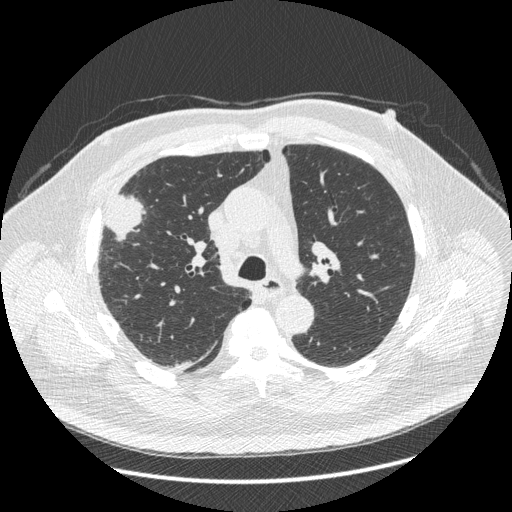
Low-dose screening chest CT, one axial slice; slice 284 of 426 in the series (ordered by position); reconstruction kernel STANDARD; 120 kVp; lung window (W 1500 / L -600 HU); 1.25 mm slice thickness; 512 × 512 image matrix, field of view 400 × 400 mm.
Outlined on this slice (expert manual segmentation):
- lesion 1 (tumor, upper lobe of right lung): bounding box <106,195,143,236> (left, top, right, bottom; pixels)